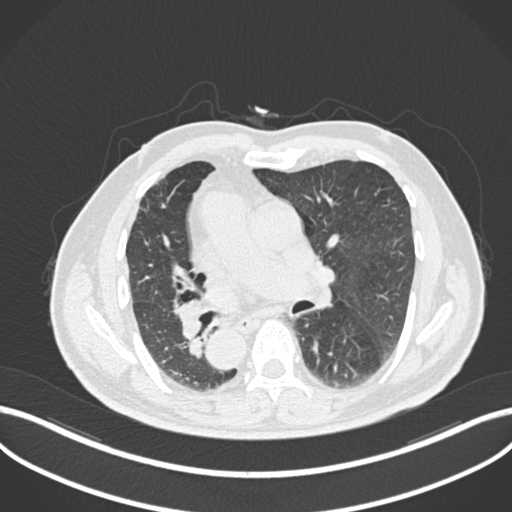
Chest CT, one axial slice; position 119 of 206 along the scan axis; 120 kVp; lung window (W 1500 / L -600 HU); 1 mm slice thickness; 512 × 512 image matrix. Patient: male, 67 years. Case-level facts recorded for this patient, not image findings: clinical TNM (as recorded): T2a N0 M0.
Outlined on this slice (rectangle marked by the reading radiologist):
- lung tumour (recorded histology: squamous cell carcinoma): box from (x=170, y=297) to (x=207, y=342) px